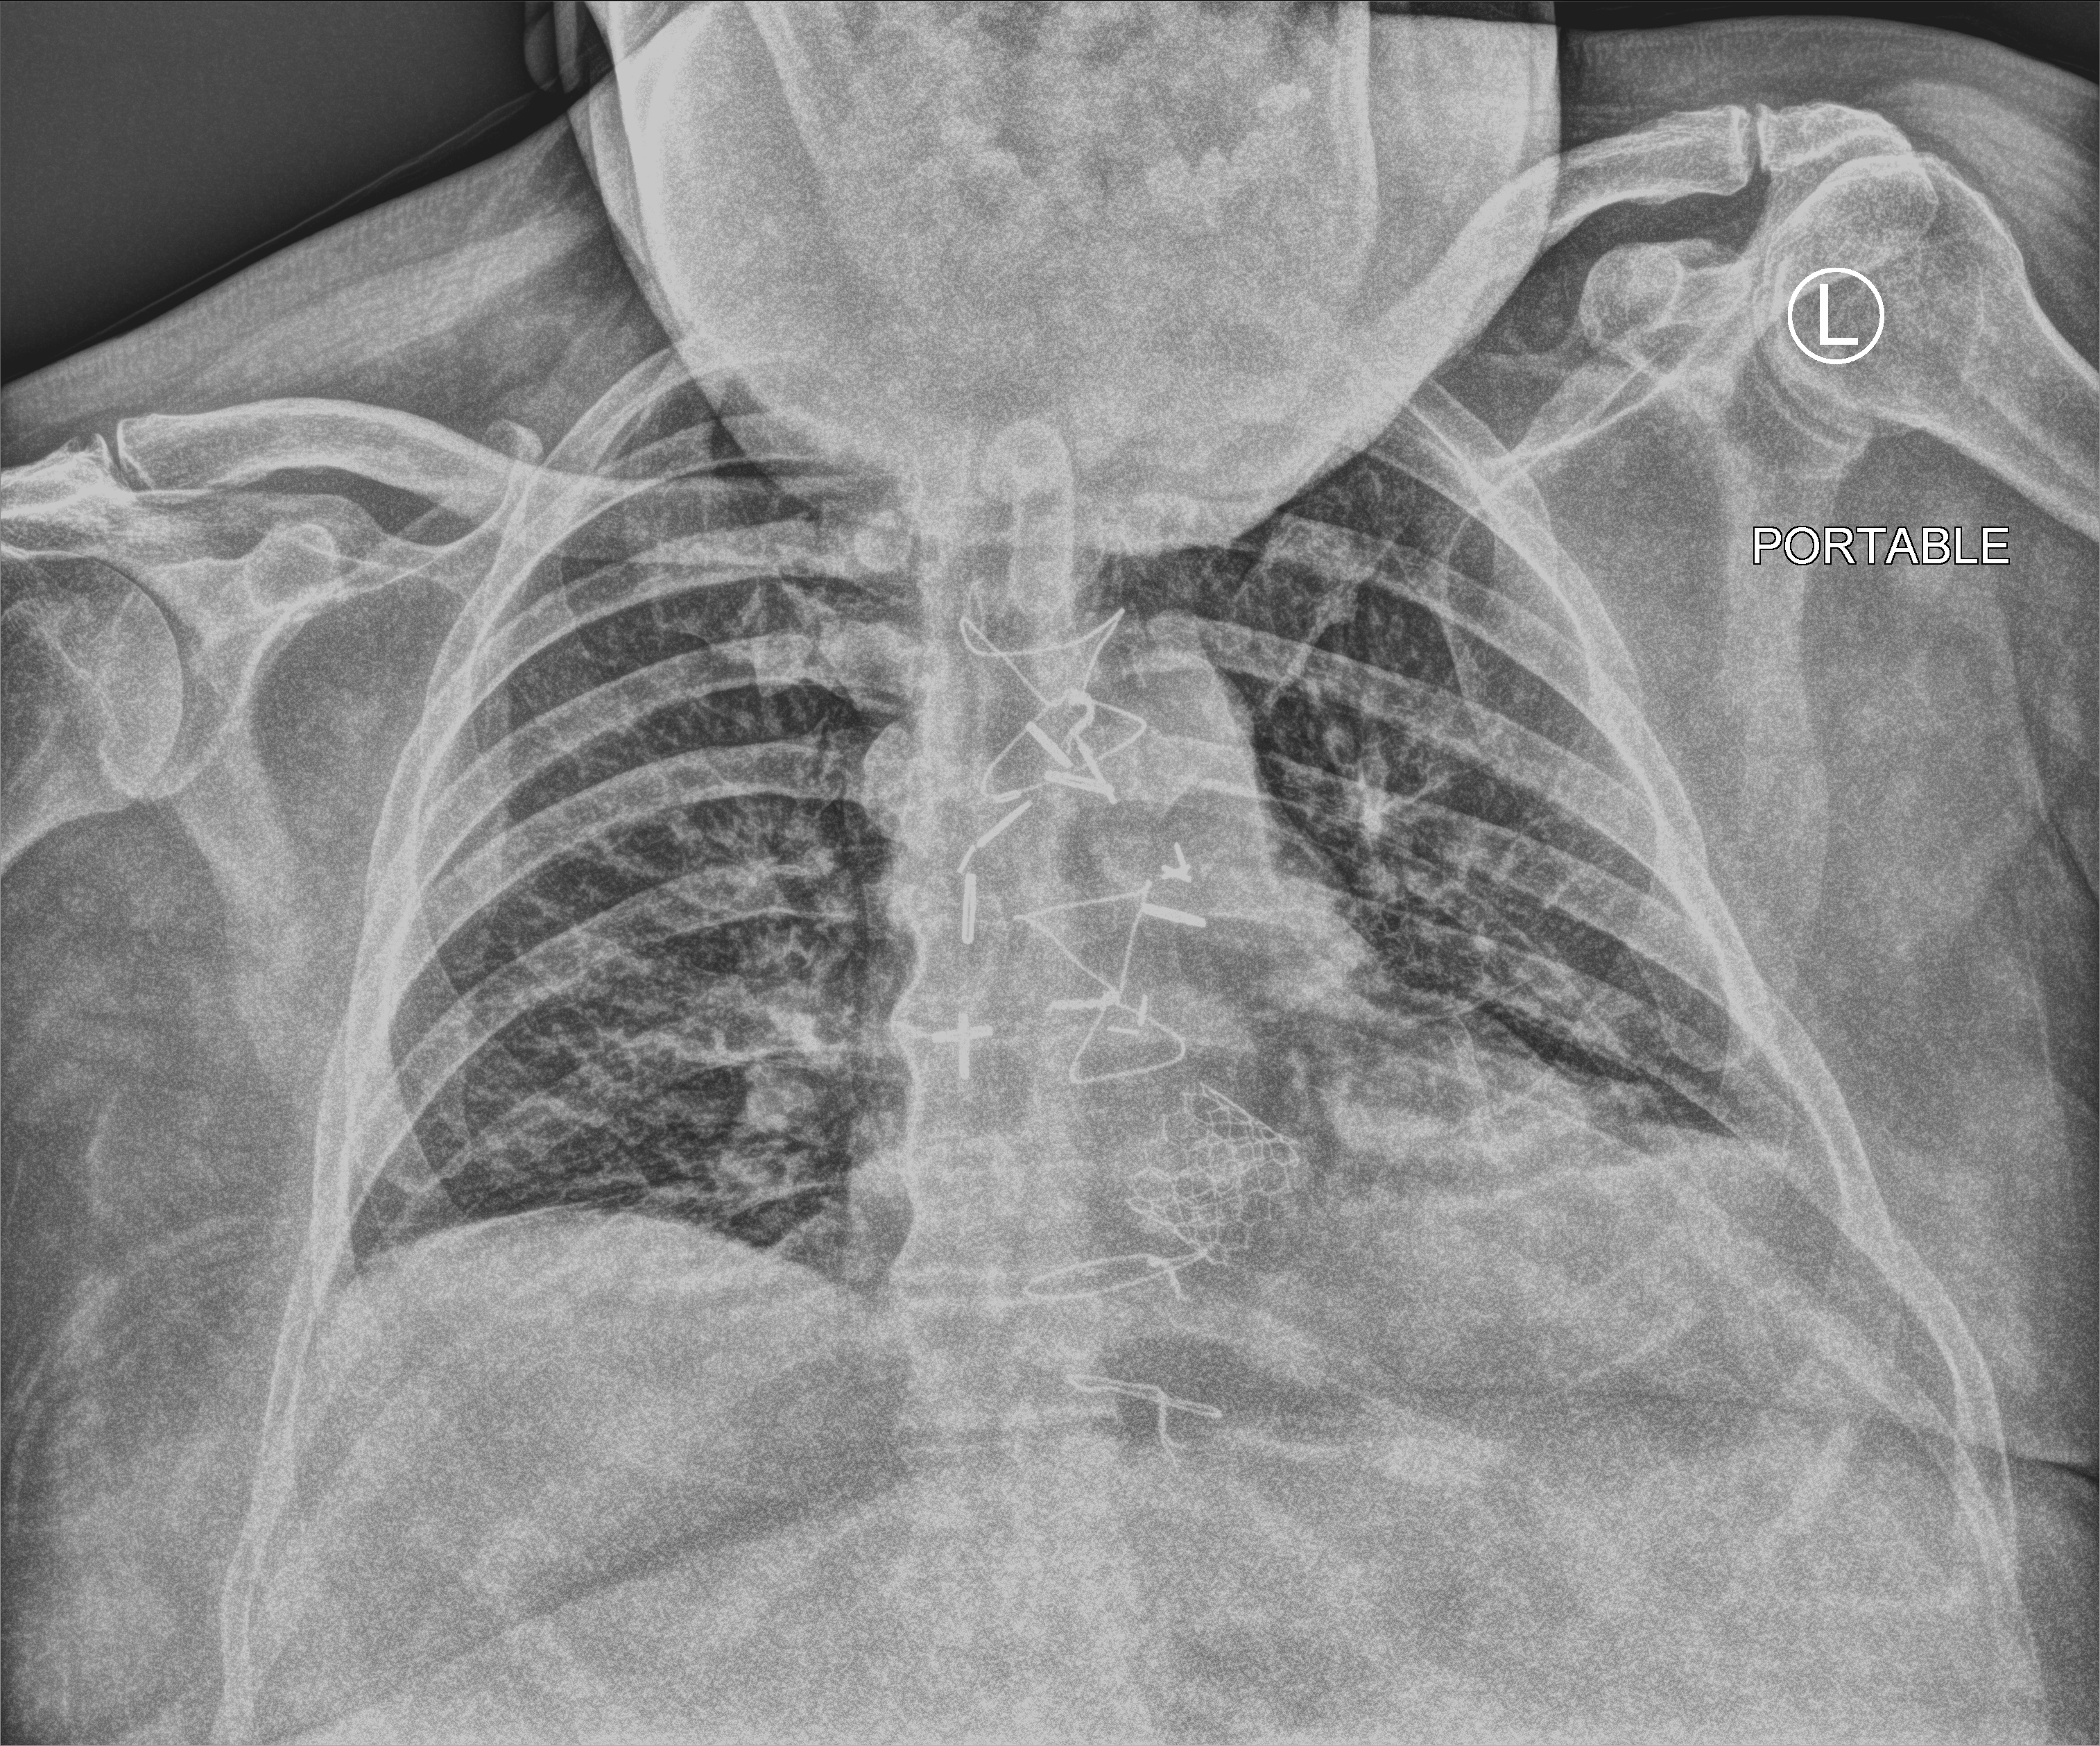
Portable chest radiograph, anteroposterior (AP) projection. Patient hospitalised with COVID-19; male, aged 60–74 years.
From the hospital-stay record, not from the radiograph (when in the stay this image was taken is not recorded):
- mechanically ventilated during this hospital stay: yes